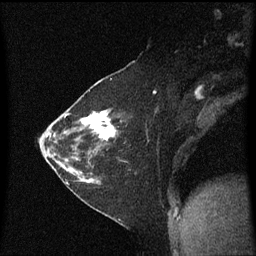
Breast MRI (dynamic contrast-enhanced), one sagittal slice. Slice 33 of 60 in the series (ordered by position). Dynamic contrast-enhanced series, image 2 of 3 at this slice position (ordered by acquisition). 1.5 T. TE 4.2 ms, TR 8.4 ms. 256 × 256 image matrix, field of view 200 × 200 mm. Patient: female, 36 years. From the clinical record (not read from this slice): setting: breast cancer imaged before/during neoadjuvant chemotherapy; receptor status: HR-positive, HER2-negative.
Structures marked on this image (semi-automatic segmentation, software-assisted and operator-edited):
- analysis volume of interest (the breast-tissue region the enhancement analysis was run in; not a lesion): bounding box <66,102,119,179> (left, top, right, bottom; pixels)
- tumour enhancement mask (voxels above the 70 % enhancement threshold inside the analysis volume of interest): <67,110,117,141>